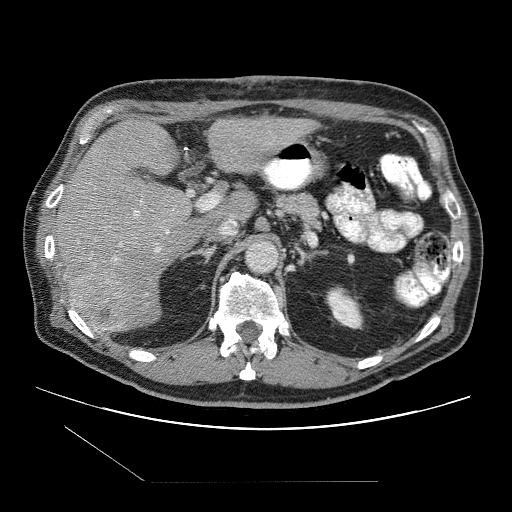
Contrast-enhanced abdominal CT (liver protocol), one axial slice. Slice 56 of 109 in the series (ordered by position). Reconstruction kernel STANDARD. One of 2 acquisitions stored at this slice position. Soft-tissue window (W 400 / L 40 HU). 2.5 mm slice thickness. 512 × 512 image matrix, field of view 400 × 400 mm. From the clinical record (not read from this slice): diagnosis: hepatocellular carcinoma (patient treated with transarterial chemoembolisation; whether this scan precedes or follows treatment is not stated here); TNM stage (as recorded): Stage-IIIB.
Outlined on this slice (semi-automatic segmentation, software-assisted and operator-edited):
- liver parenchyma outside the tumour (the mass and vessels are separate outlines, so this box may not span the whole liver): bounding box <54,118,315,331> (left, top, right, bottom; pixels)
- mass: <69,269,137,327>
- liver vessels: <114,200,169,260>